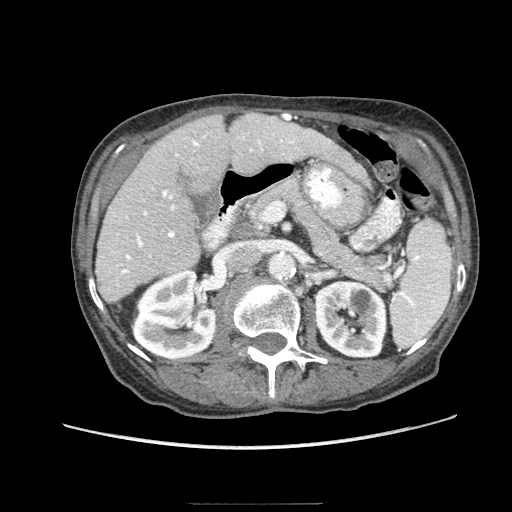
Contrast-enhanced abdominal CT (liver protocol), one axial slice; slice 39 of 83 in the series (ordered by position); reconstruction kernel STANDARD; 140 kVp; soft-tissue window (W 400 / L 40 HU); 2.5 mm slice thickness; 512 × 512 image matrix, field of view 360 × 360 mm. Case-level facts recorded for this patient, not image findings: diagnosis: hepatocellular carcinoma (patient treated with transarterial chemoembolisation; whether this scan precedes or follows treatment is not stated here); TNM stage (as recorded): Stage-I; Child-Pugh class: A.
Outlined on this slice (semi-automatic segmentation, software-assisted and operator-edited):
- liver parenchyma outside the tumour (the mass and vessels are separate outlines, so this box may not span the whole liver): bounding box <96,112,344,302> (left, top, right, bottom; pixels)
- liver vessels: <117,133,294,286>